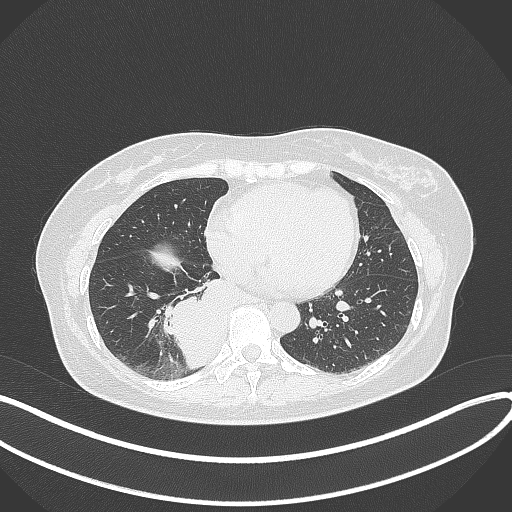
Chest CT, one axial slice; slice 129 of 331 in the series (ordered by position); reconstruction kernel B70f; lung window (W 1500 / L -600 HU); 1 mm slice thickness; 512 × 512 image matrix, field of view 400 × 400 mm. Female patient, age 54 years. Case-level facts recorded for this patient, not image findings: clinical TNM (as recorded): T4 N0 M0.
Structures marked on this image (rectangle marked by the reading radiologist):
- lung tumour (recorded histology: adenocarcinoma): bounding box [x1, y1, x2, y2] px = [163, 271, 233, 377]